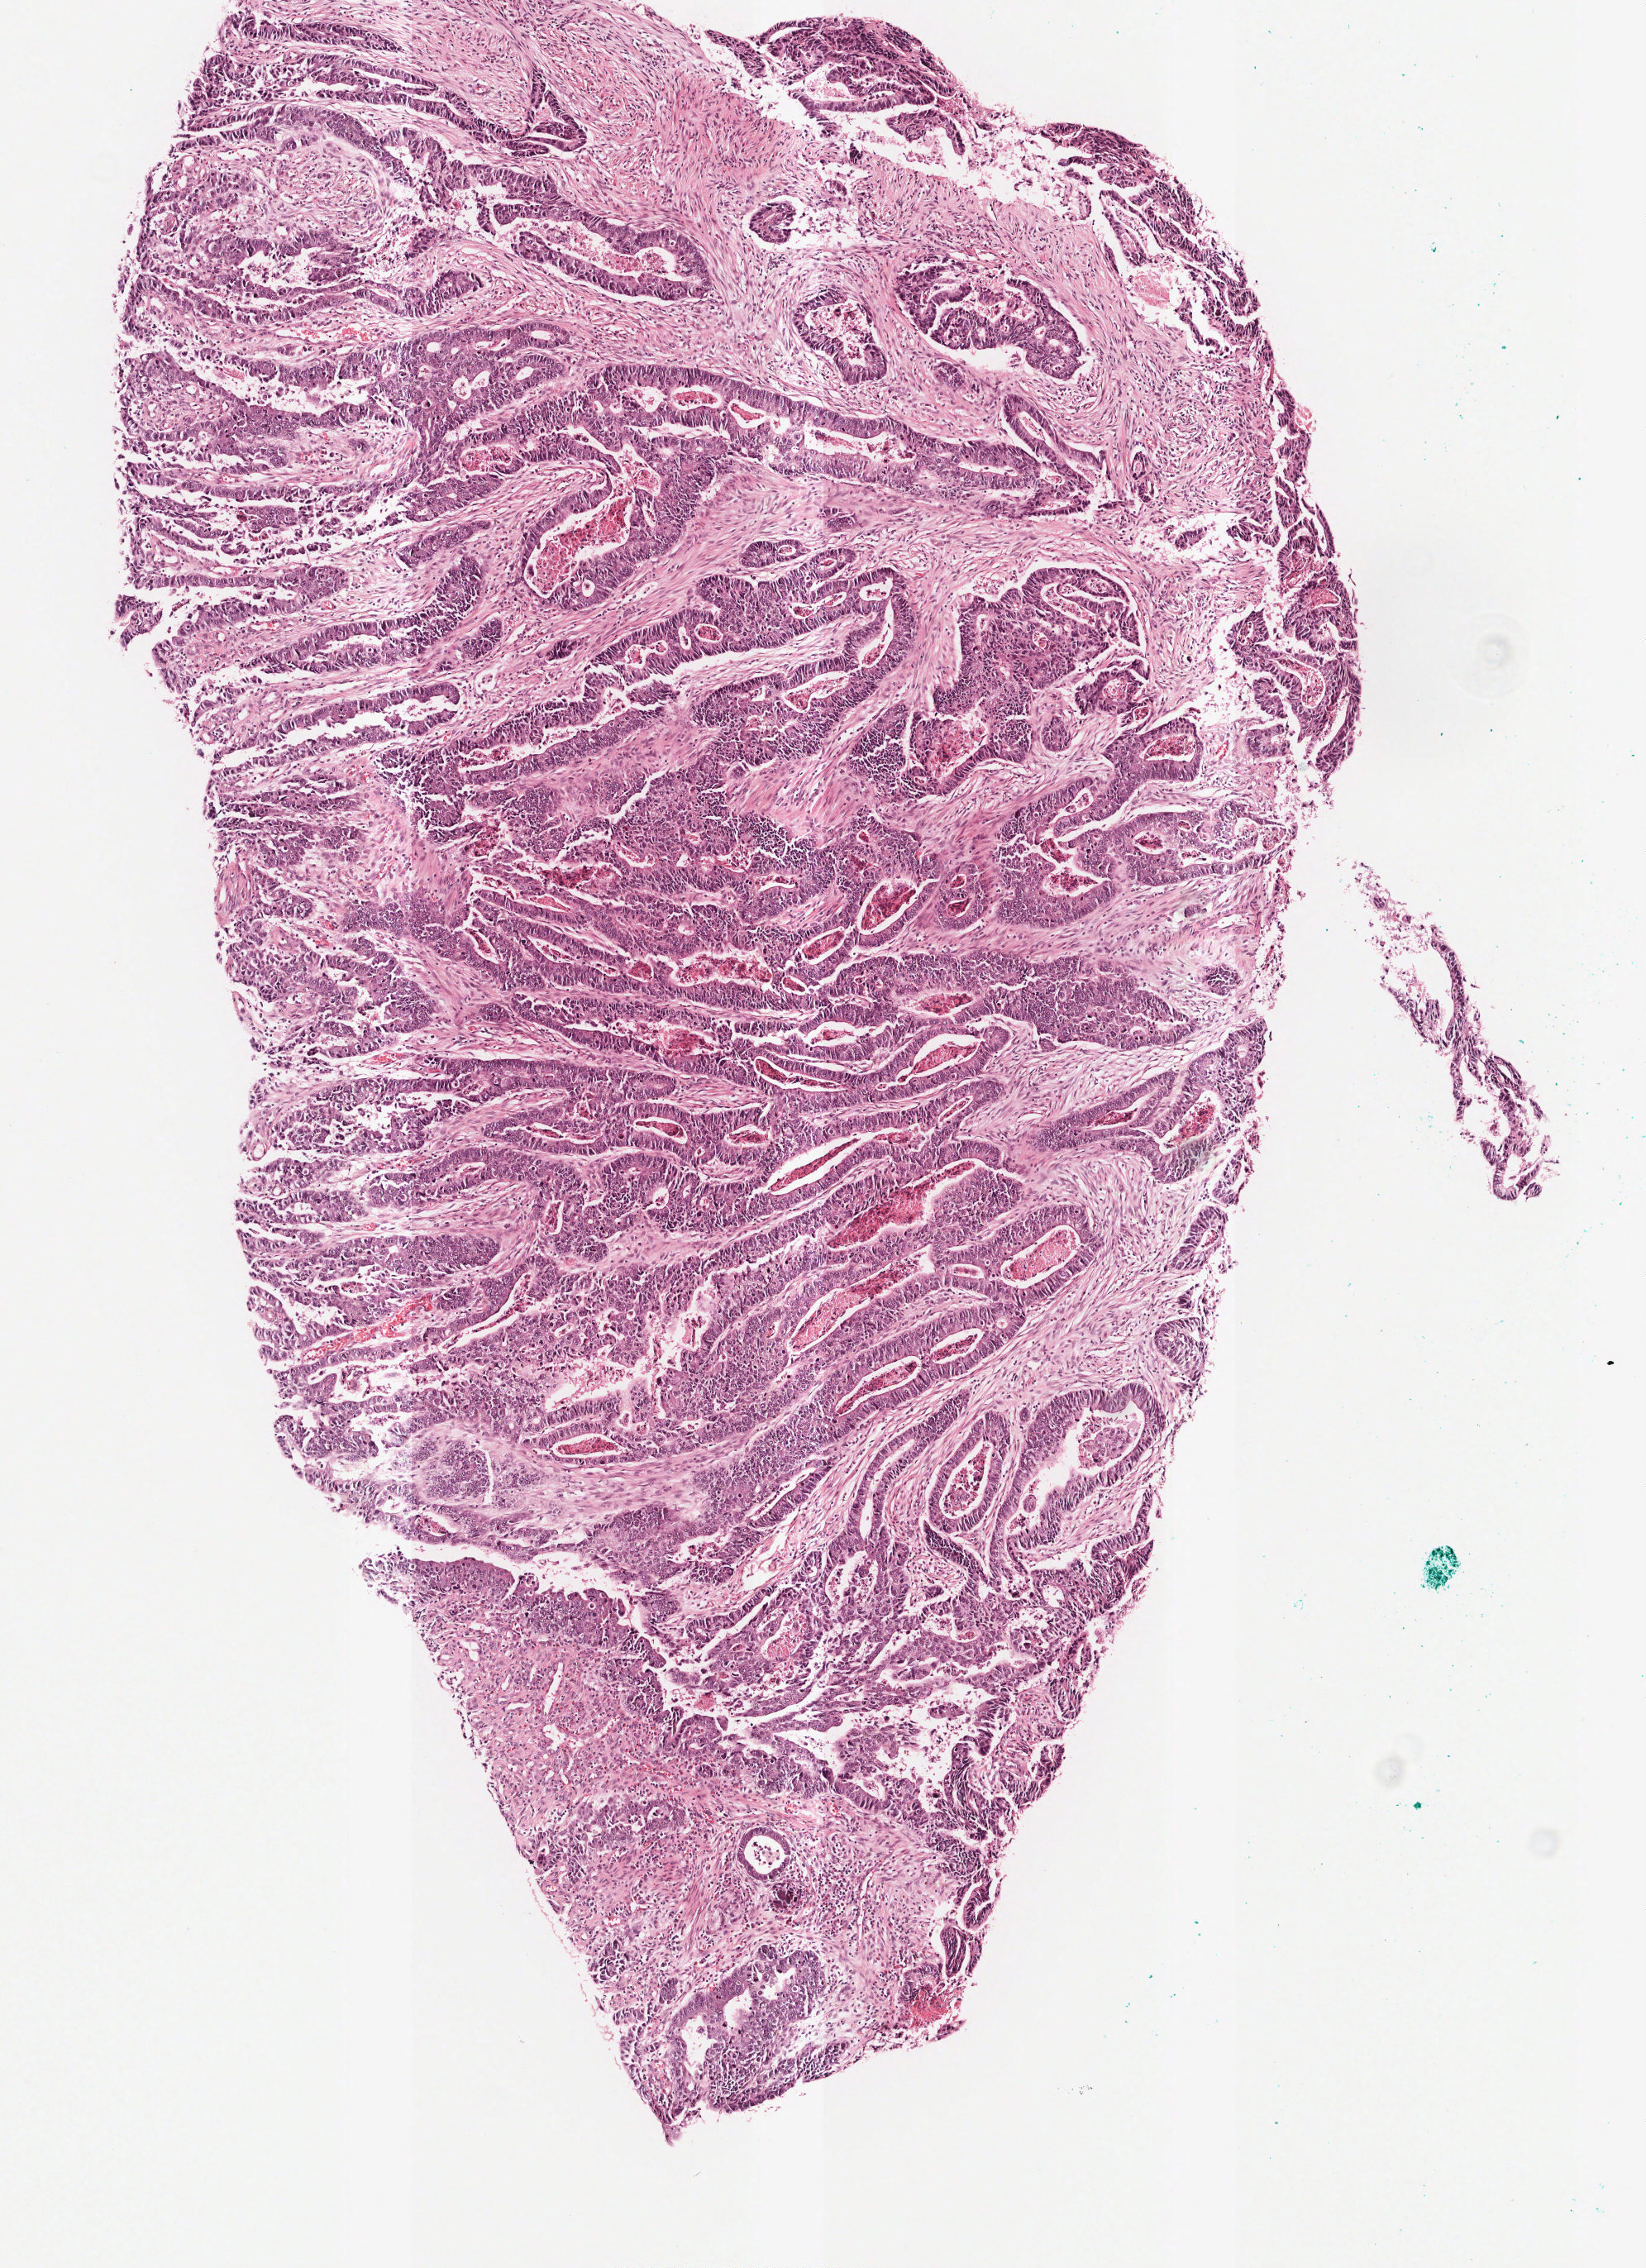
Whole-slide histology image, H&E — low-resolution overview of the scanned area, about 3.9 x 5.4 mm, FFPE section, stomach, primary tumour sample. Male patient; age at initial diagnosis 56 years. Histologic grade: G3 (poorly differentiated).
AJCC pathologic stage: IIB (7th edition). Lymph nodes positive (case pathology): 1 of 40 examined. Histologic diagnosis: Tubular adenocarcinoma (gastric antrum).